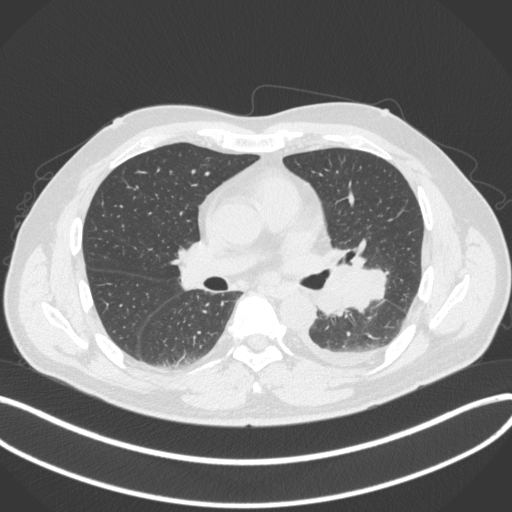
Chest CT, one axial slice. Slice 197 of 350 in the series (ordered by position). Reconstruction kernel B31f. 120 kVp. Lung window (W 1500 / L -600 HU). 1 mm slice thickness. 512 × 512 image matrix, field of view 400 × 400 mm. Male patient, age 58 years. Case-level facts recorded for this patient, not image findings: clinical TNM (as recorded): T3 N1 M1b; histopathological grade: G3.
Annotated regions visible in this slice (rectangle marked by the reading radiologist):
- lung tumour (recorded histology: small cell carcinoma): bounding box (x1, y1, x2, y2) in pixels: (316, 258, 389, 317)